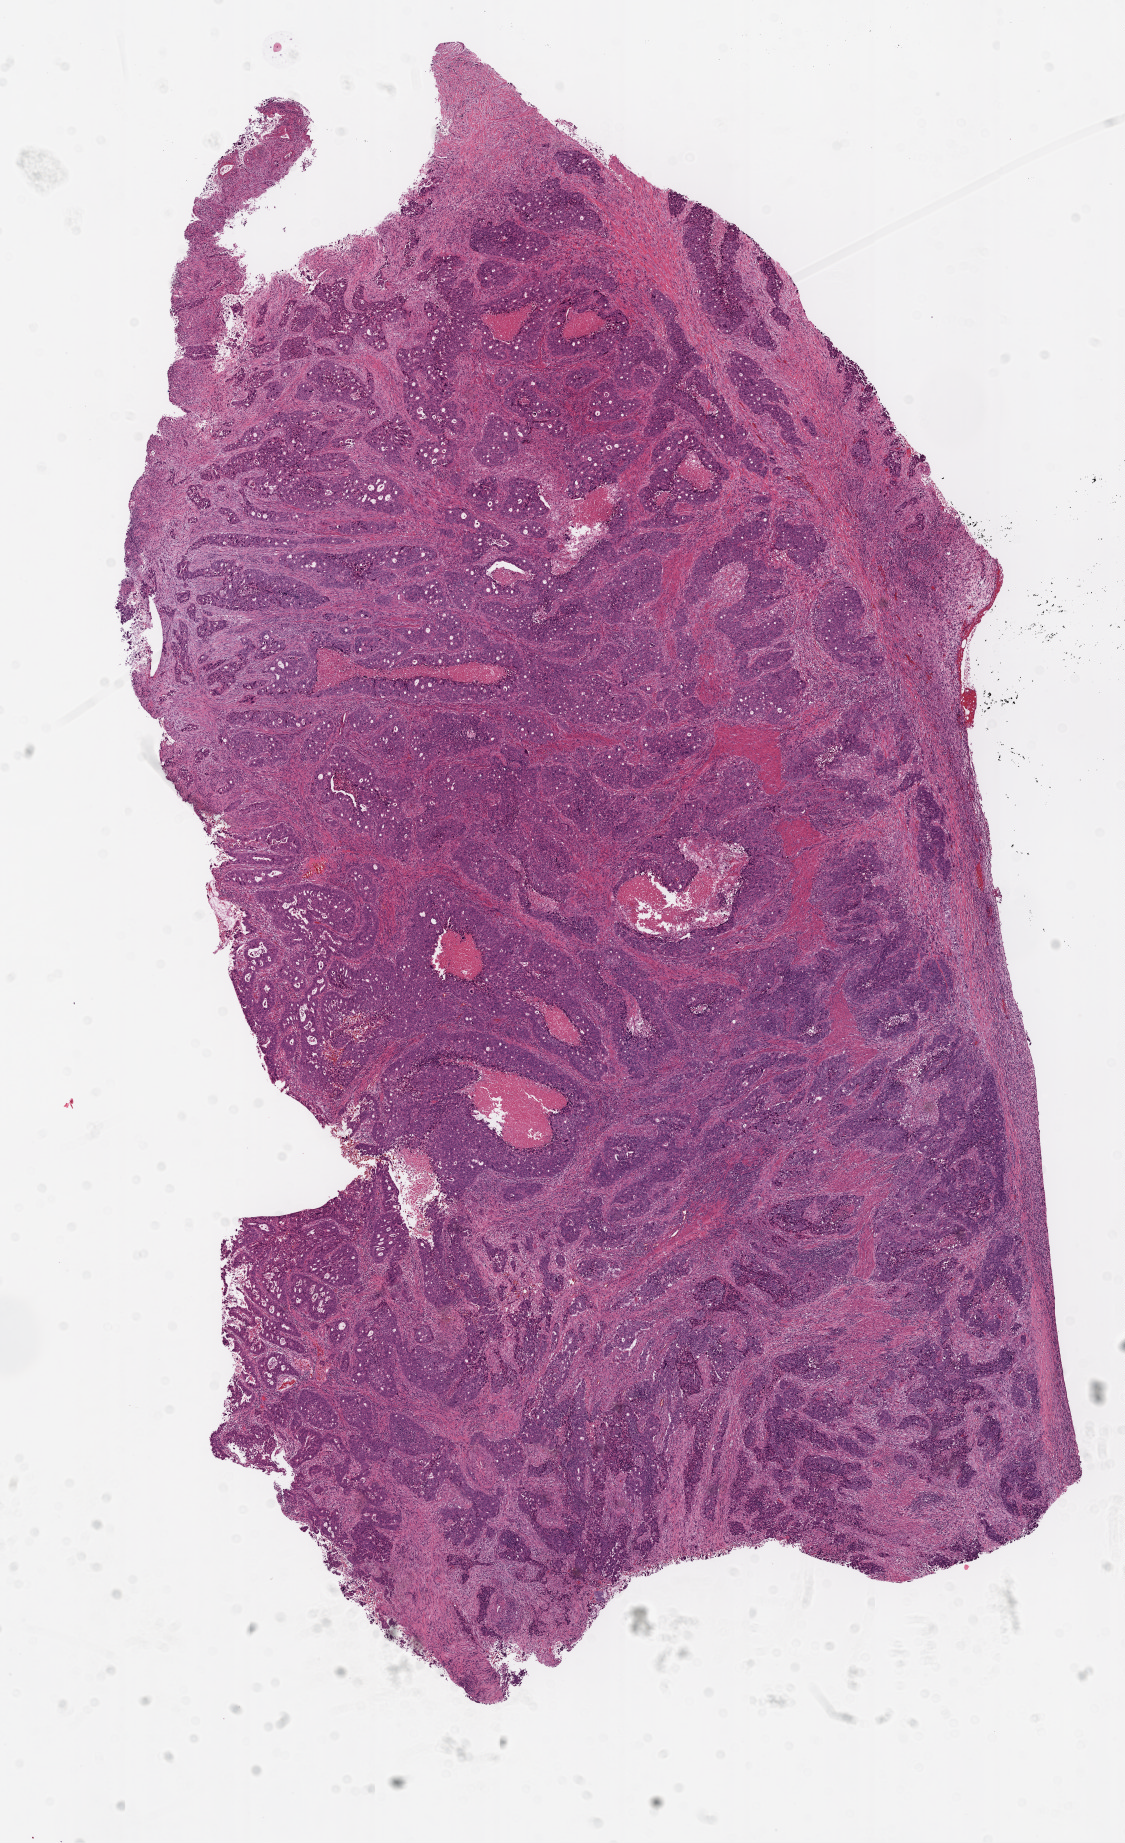
Whole-slide histology image, H&E, a low-resolution overview of the entire scanned area, about 9.0 x 14.8 mm (slide scanned at 20x), frozen section from the top of the tissue portion, colon, primary tumour sample. Patient: female, age at initial diagnosis 81 years. Composition of this section per pathologist review: tumour cells 82%, tumour nuclei 80%, normal cells 0%, stromal cells 10%, necrosis 8%.
TNM: T3 N0 M0. AJCC pathologic stage: IIA. Diagnosis: Adenocarcinoma, NOS.